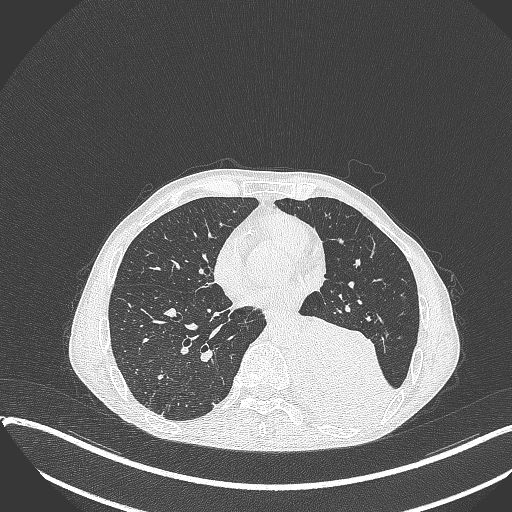
Chest CT, one axial slice. Slice 147 of 401 in the series (ordered by position). Reconstruction kernel B70f. 120 kVp. Lung window (W 1500 / L -600 HU). 512 × 512 image matrix, field of view 400 × 400 mm. Patient: male, 57 years. Case-level facts recorded for this patient, not image findings: clinical TNM (as recorded): T4 N0 M0.
Outlined on this slice (bounding box drawn by a radiologist):
- lung tumour (recorded histology: squamous cell carcinoma): box from (x=295, y=314) to (x=396, y=427) px